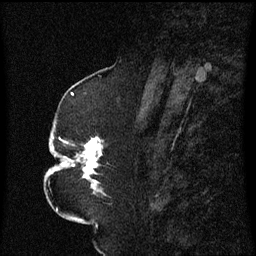
Breast MRI (dynamic contrast-enhanced), one sagittal slice; slice 28 of 60 in the series (ordered by position); dynamic contrast-enhanced series, image 2 of 3 at this slice position (ordered by acquisition); 1.5 T; TE 4.2 ms, TR 8.4 ms; 256 × 256 image matrix. Female patient, age 52 years. Case-level facts recorded for this patient, not image findings: setting: breast cancer imaged before/during neoadjuvant chemotherapy; receptor status: HR-positive, HER2-negative.
Structures marked on this image (semi-automatic segmentation, software-assisted and operator-edited):
- analysis volume of interest (the breast-tissue region the enhancement analysis was run in; not a lesion): bounding box (x1, y1, x2, y2) in pixels: (49, 124, 109, 197)
- tumour enhancement mask (voxels above the 70 % enhancement threshold inside the analysis volume of interest): (61, 138, 103, 189)